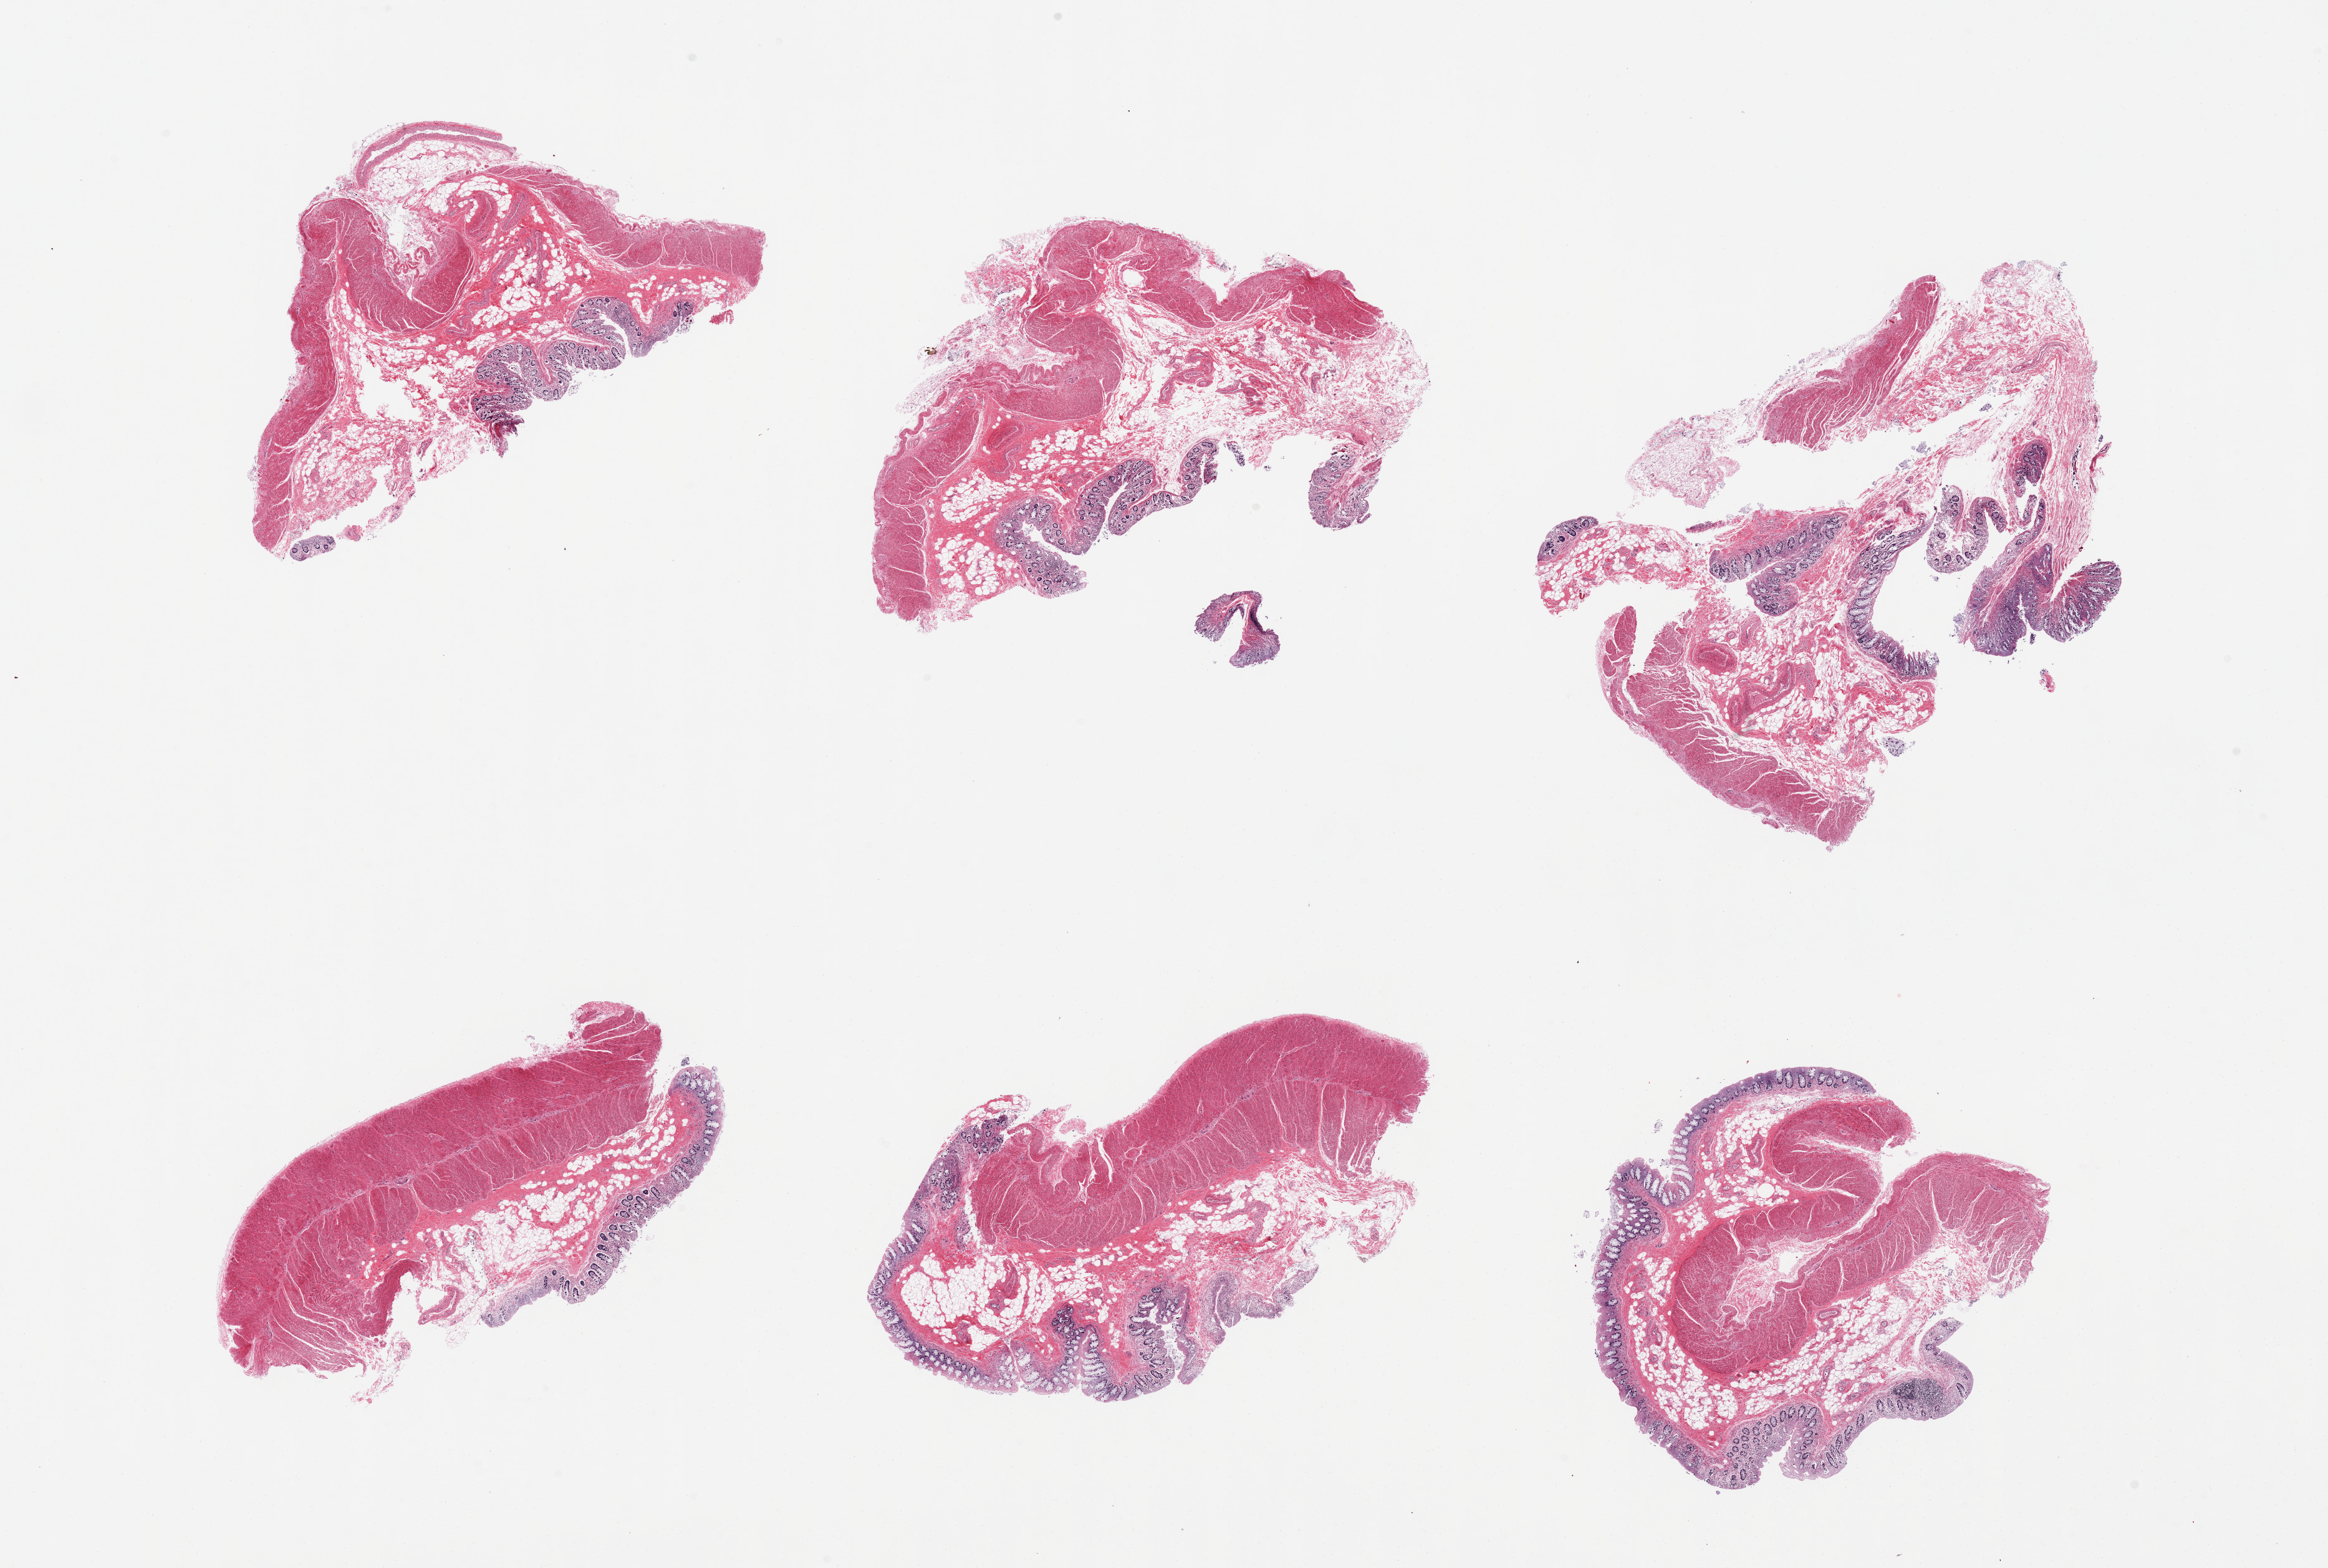
Digitized hematoxylin and eosin (H&E)-stained section, shown as a low-resolution overview of the whole scanned area (about 29.5 x 19.9 mm, from a 20x scan); PAXgene-fixed, paraffin-embedded tissue; target tissue: transverse colon; donor tissue sample.
• reviewer comment on this tissue sample: 6 pieces, includes muscularis and severely autolyzed mucosa